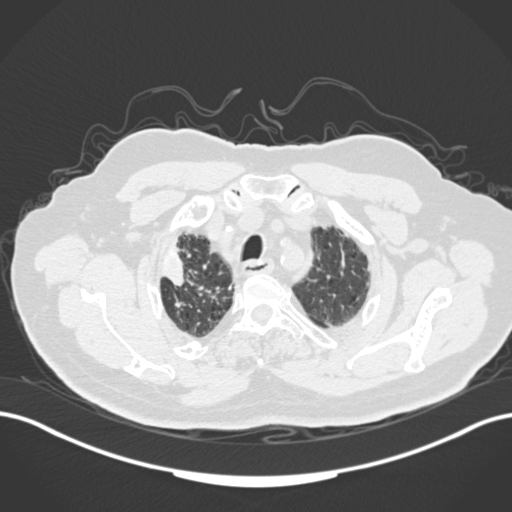
Chest CT, one axial slice; position 145 of 205 along the scan axis; lung window (W 1500 / L -600 HU); 1 mm slice thickness; 512 × 512 image matrix, field of view 400 × 400 mm. Male patient, age 72 years. Case-level facts recorded for this patient, not image findings: clinical TNM (as recorded): T1a N0 M0.
Annotated regions visible in this slice (rectangle marked by the reading radiologist):
- lung tumour (recorded histology: squamous cell carcinoma): bounding box (x1, y1, x2, y2) in pixels: (163, 237, 190, 288)